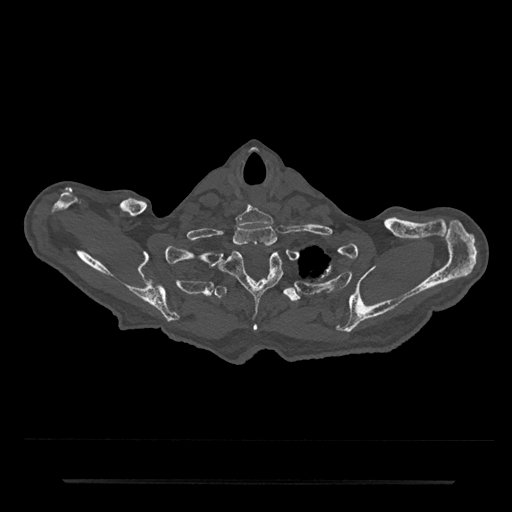
CT including the spine, one axial slice; slice 698 of 797 in the series (ordered by position); reconstruction kernel Br40s/3; bone window (W 1800 / L 400 HU); 512 × 512 image matrix, field of view 427 × 427 mm. Male patient, age 74 years. Case-level facts recorded for this patient, not image findings: primary cancer: prostate.
Outlined on this slice (semi-automatic segmentation, software-assisted and operator-edited):
- T1 vertebra: bounding box [x1, y1, x2, y2] px = [233, 225, 277, 248]
- T2 vertebra: [217, 251, 283, 331]
- T3 vertebra: [214, 285, 301, 302]